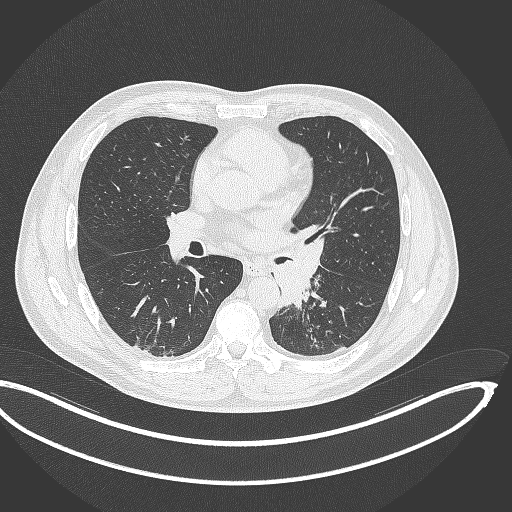
Chest CT, one axial slice. Slice 188 of 362 in the series (ordered by position). Reconstruction kernel B70f. 120 kVp. Lung window (W 1500 / L -600 HU). 1 mm slice thickness. 512 × 512 image matrix. Patient: male, 50 years. From the clinical record (not read from this slice): clinical TNM (as recorded): T2a N3 M0.
Outlined on this slice (bounding box drawn by a radiologist):
- lung tumour (recorded histology: squamous cell carcinoma): bounding box [x1, y1, x2, y2] px = [270, 235, 325, 311]